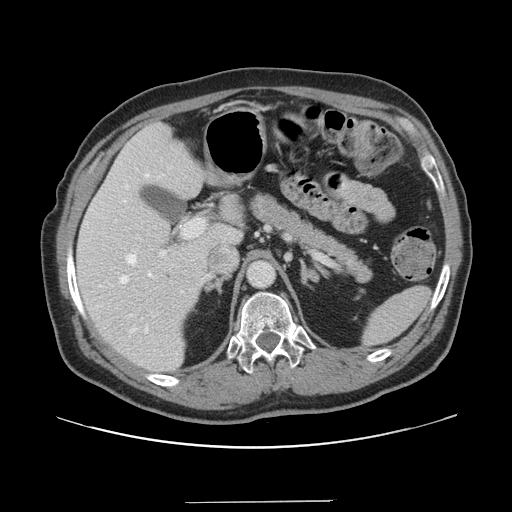
Contrast-enhanced abdominal CT, one axial slice; position 94 of 151 along the scan axis; 120 kVp; intravenous contrast given; soft-tissue window (W 400 / L 40 HU); 512 × 512 image matrix, field of view 399 × 399 mm. Male patient, age 63 years. From the clinical record (not read from this slice): diagnosis: colorectal cancer liver metastases, imaged before liver resection; multiple liver metastases: no; largest metastasis: 2.1 cm; disease in both lobes: no.
Structures marked on this image (outlined manually by an expert reader):
- hepatic veins: box from (x=120, y=174) to (x=209, y=334) px
- liver: (x=77, y=124)–(x=241, y=373)
- planned liver remnant (the part of the liver to remain after resection): (x=76, y=124)–(x=242, y=374)
- portal vein (with intrahepatic branches): (x=159, y=218)–(x=205, y=257)